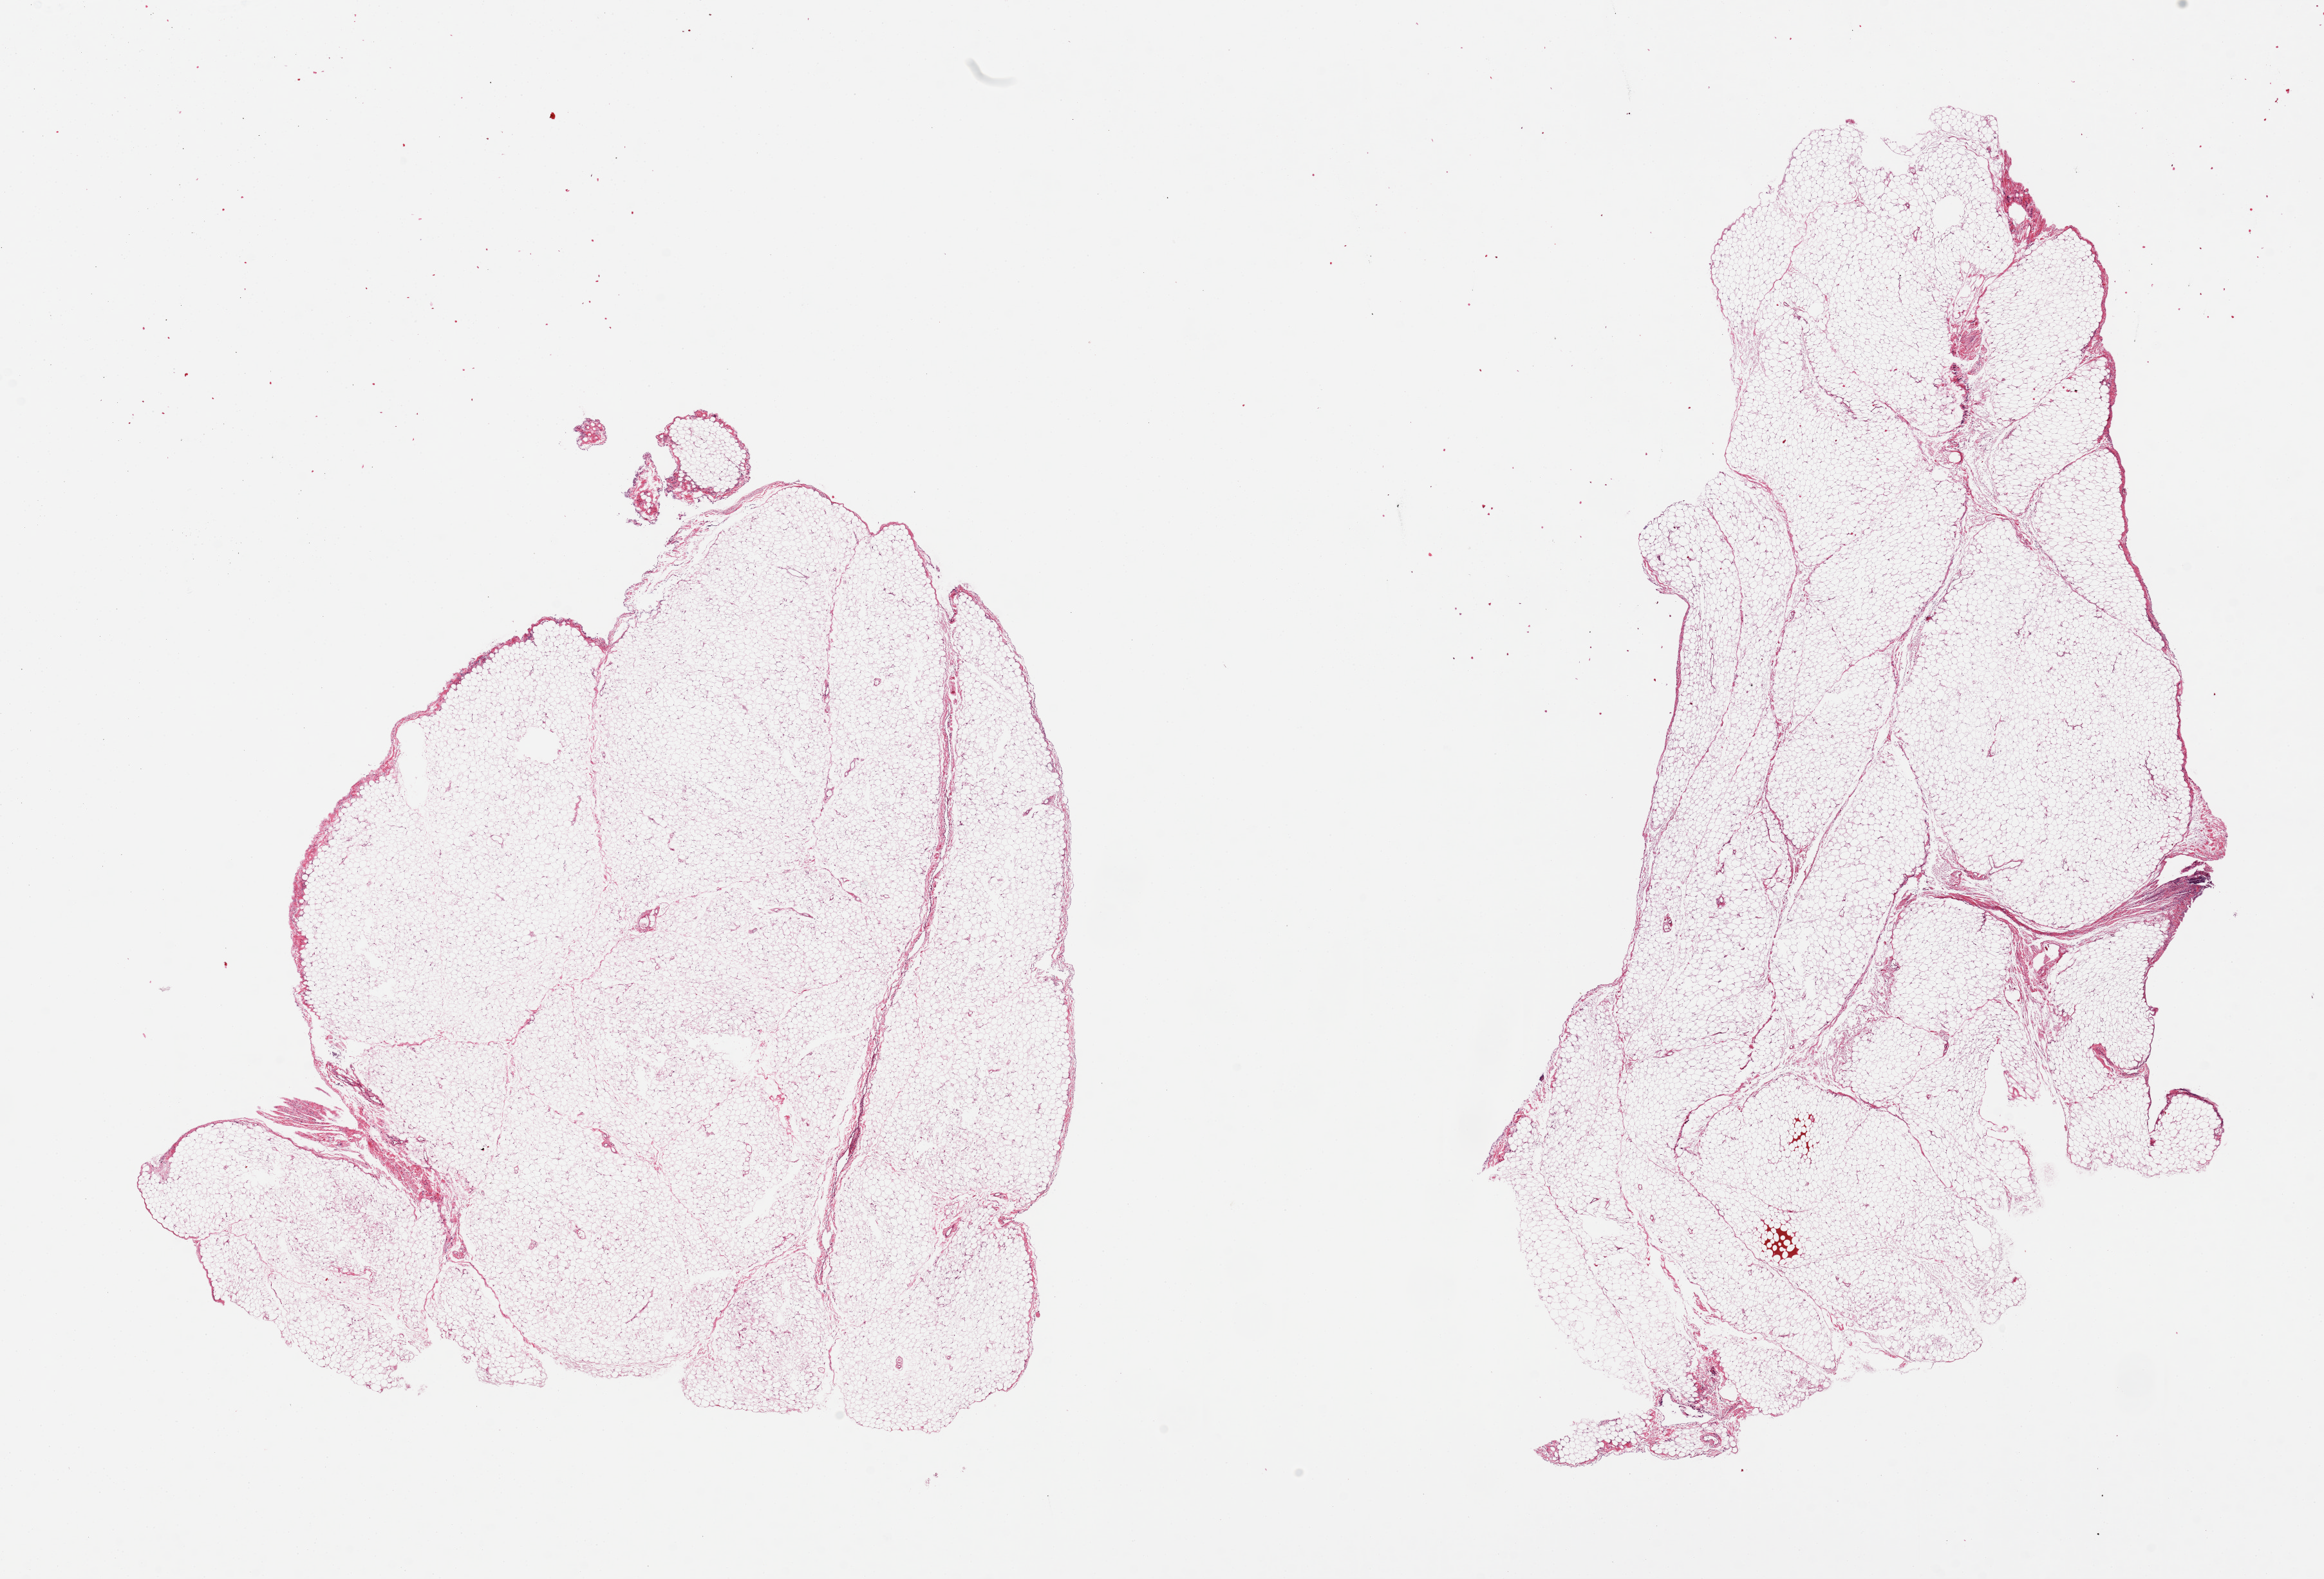
Whole-slide image, H&E stain, low-resolution overview of the scanned area, about 28.5 x 19.4 mm (slide scanned at 20x). PAXgene-fixed, paraffin-embedded tissue. Sampled site (target tissue): omentum. Donor tissue sample. Donor: male.
* reviewer comment on this tissue sample: 2 pieces